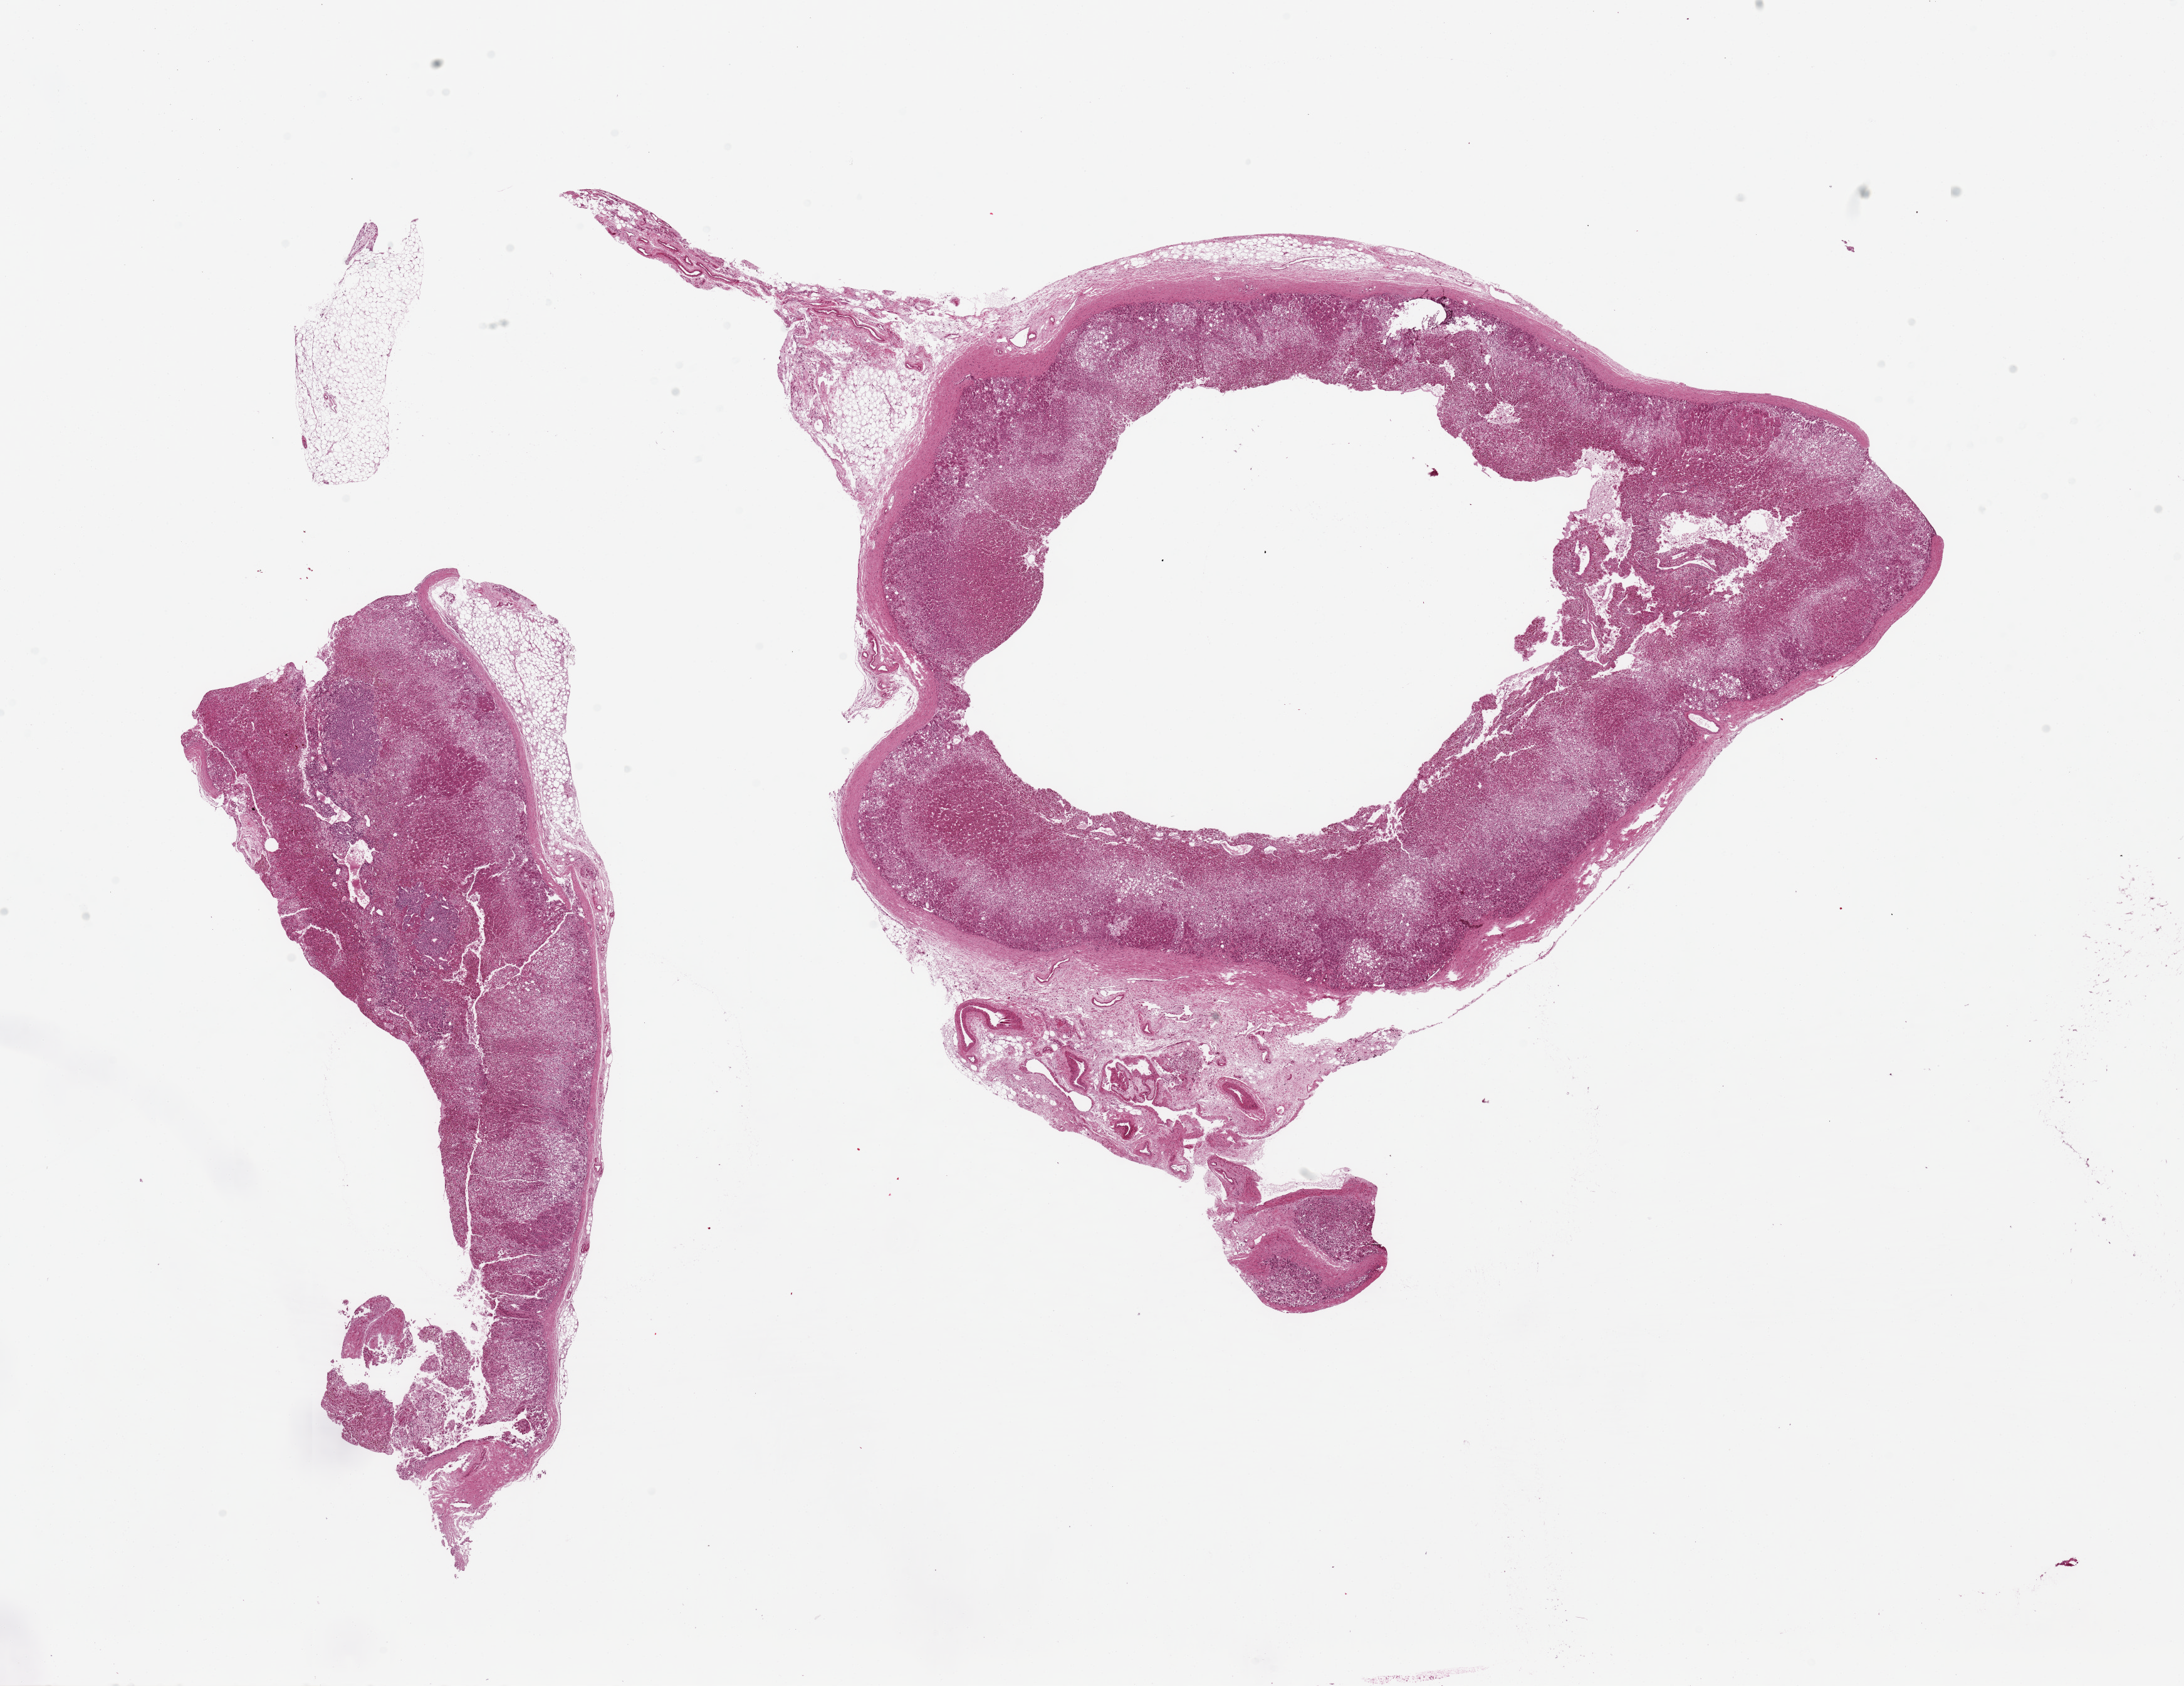
Digitized H&E-stained section, a low-resolution overview of the entire scanned area, about 27.6 x 21.3 mm. PAXgene-fixed paraffin-embedded (PFPE) section. Section of adrenal gland (target tissue). Tissue donor sample. Donor: female.
Pathologist's review note for this sample: 2 pieces, 17x5 & 17x14mm; 10-20% extraadrenal adipose.